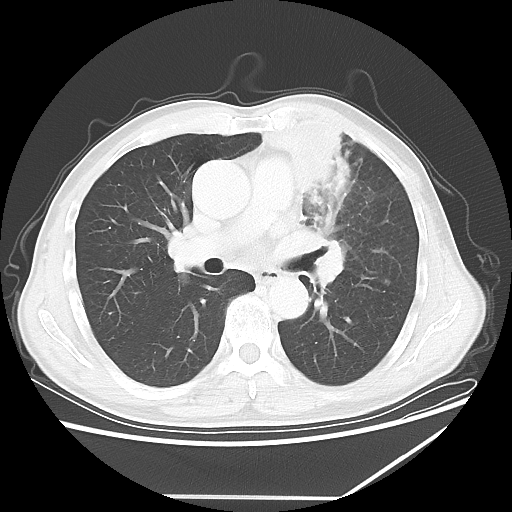
Chest CT, one axial slice; position 35 of 64 along the scan axis; lung window (W 1500 / L -600 HU); 5 mm slice thickness; 512 × 512 image matrix, field of view 383 × 383 mm. Patient: male, 64 years. From the clinical record (not read from this slice): clinical TNM (as recorded): T1c N1 M1; histopathological grade: G2.
Structures marked on this image (rectangle marked by the reading radiologist):
- lung tumour (recorded histology: squamous cell carcinoma): bounding box [x1, y1, x2, y2] px = [261, 109, 365, 242]